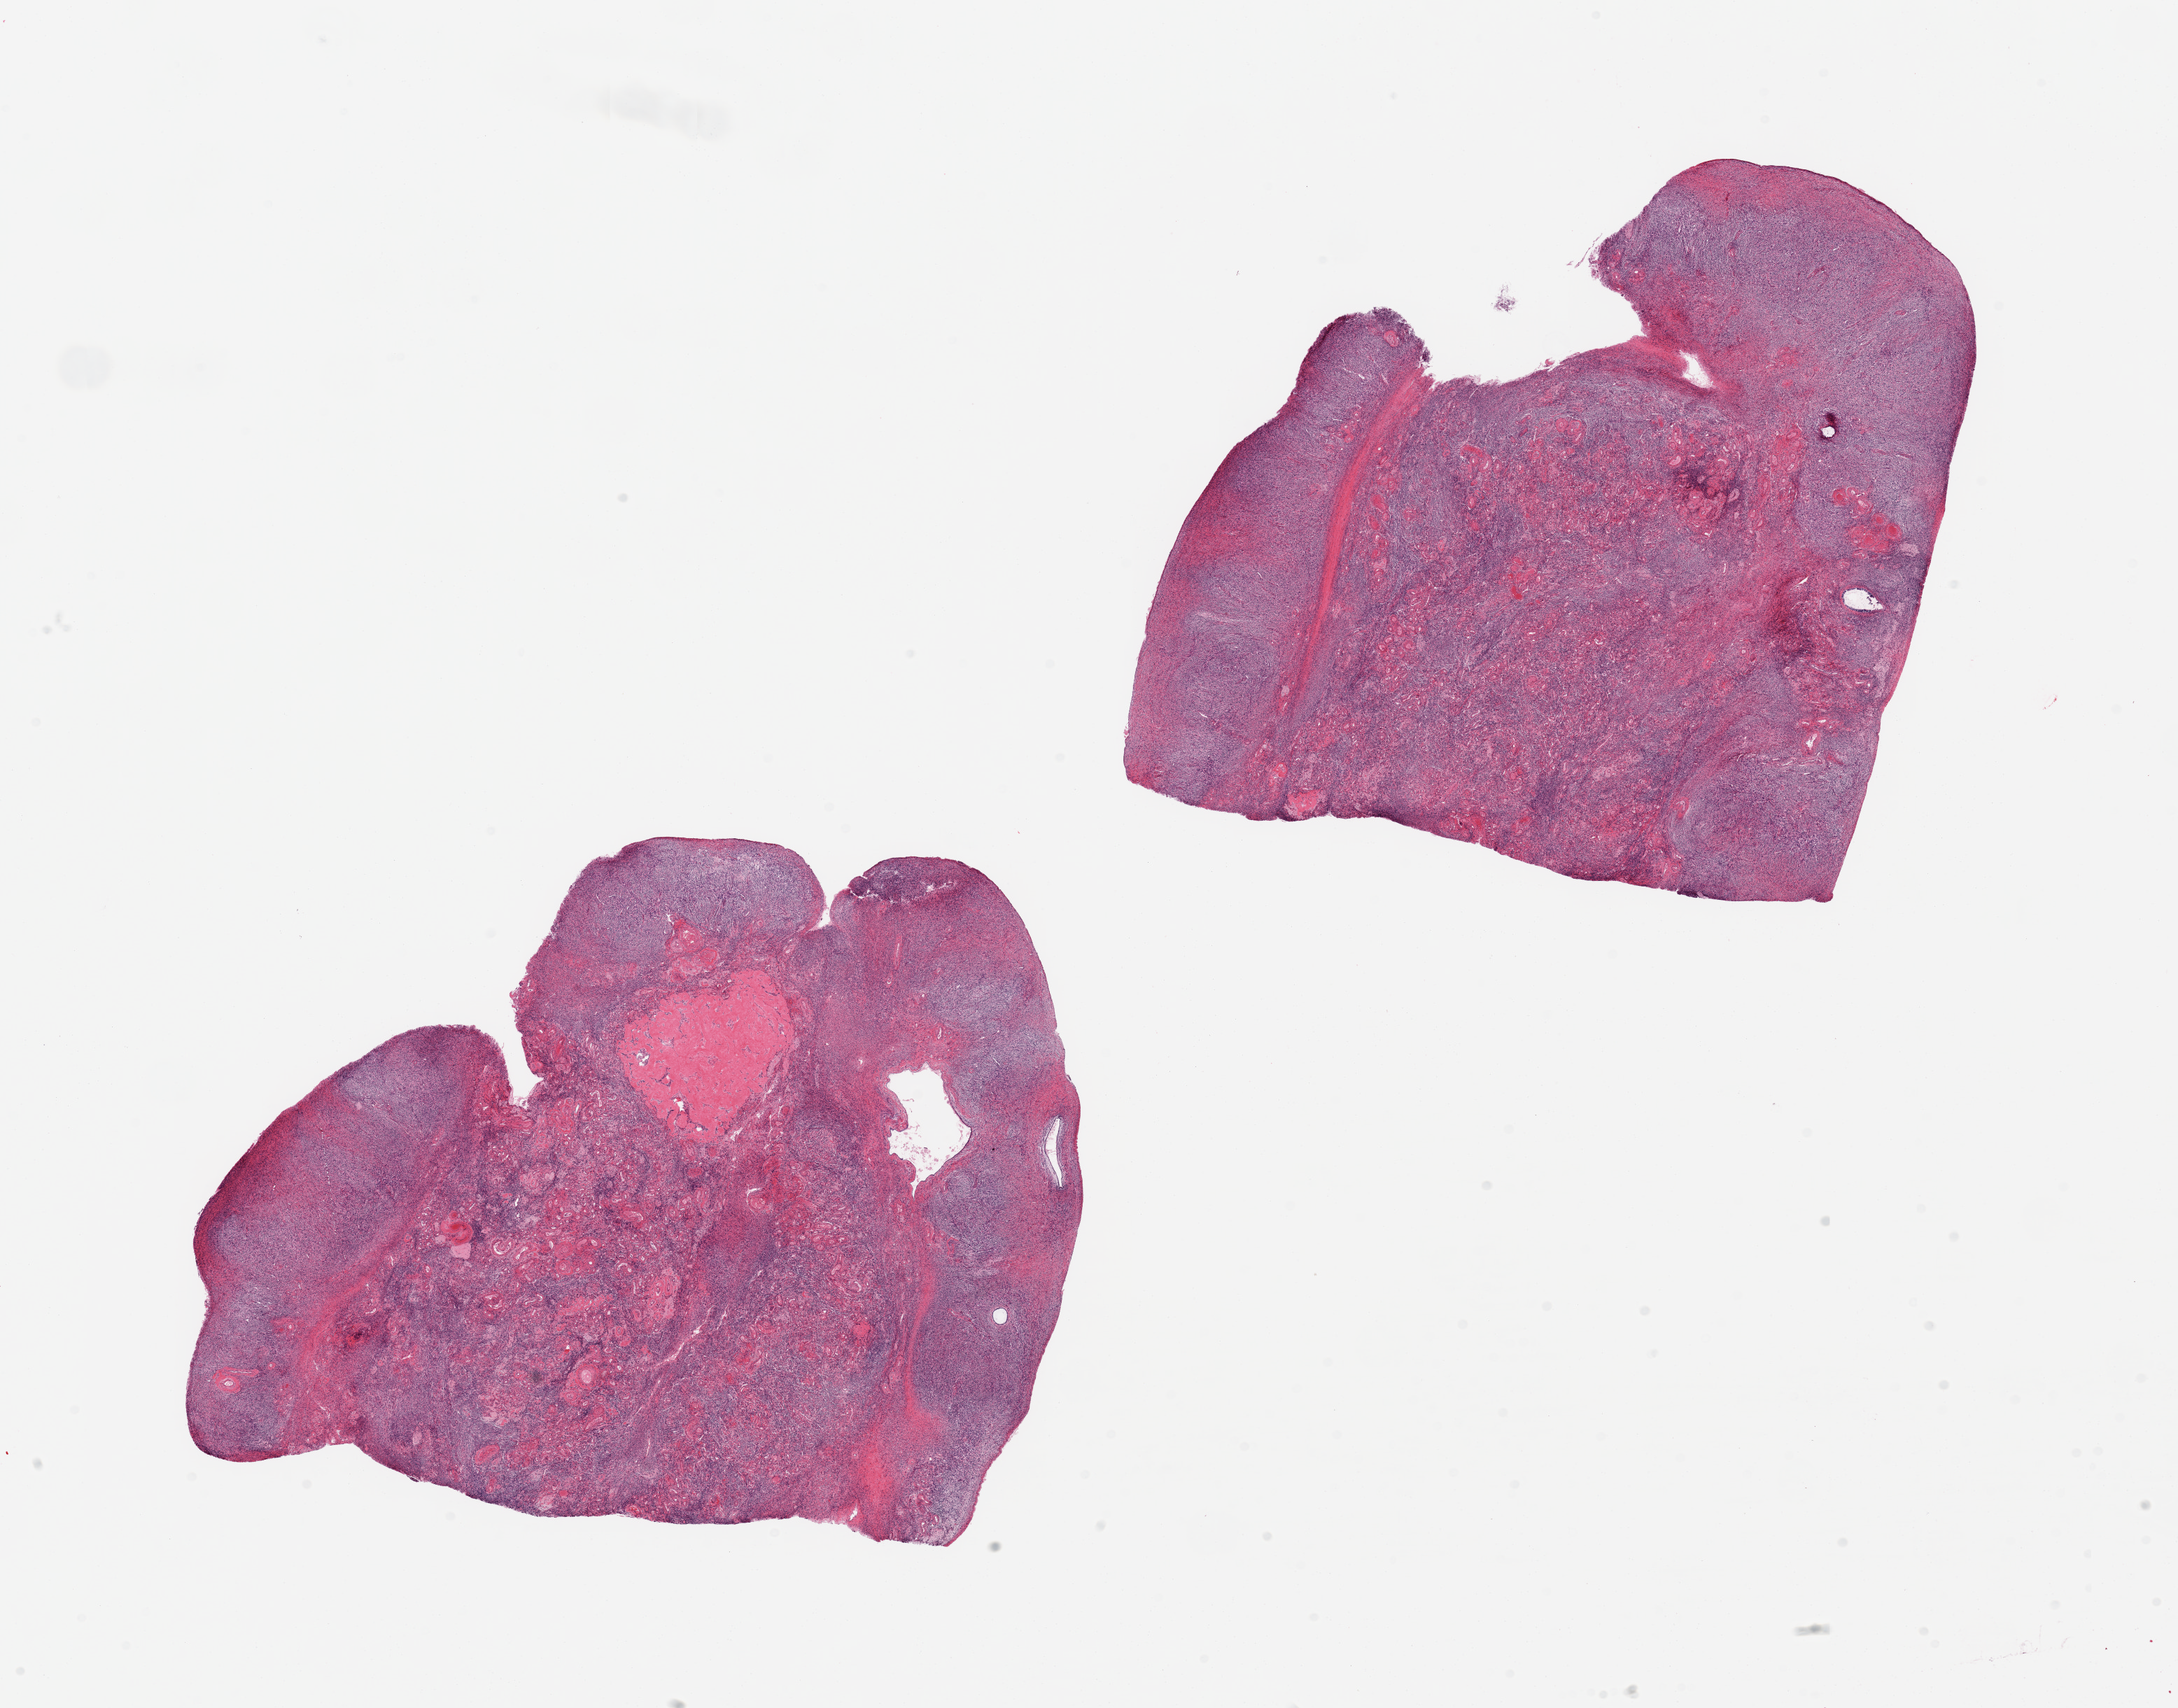
H&E whole-slide image — whole scanned area (about 24.6 x 19.3 mm) shown as a low-resolution overview, PAXgene-fixed paraffin-embedded (PFPE) section, sampled site (target tissue): ovary, donor tissue sample. Donor: female.
Reviewer comment on this tissue sample: 2 pieces; atrophic; corpora albicantia.